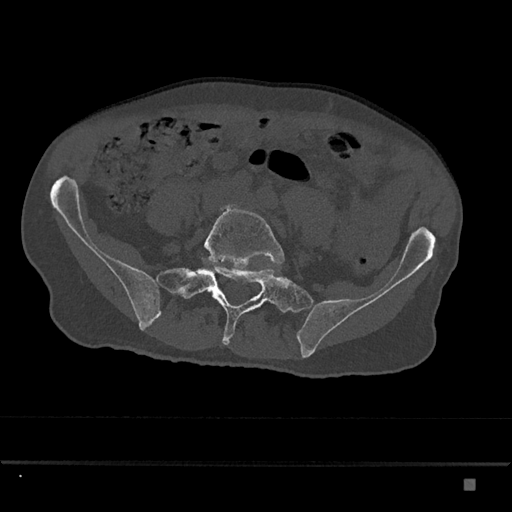
CT including the spine, one axial slice. Slice 249 of 797 in the series (ordered by position). Reconstruction kernel Br40s/3. Bone window (W 1800 / L 400 HU). 0.5 mm slice thickness. 512 × 512 image matrix, field of view 390 × 390 mm. Male patient, age 72 years. From the clinical record (not read from this slice): primary cancer: prostate.
Structures marked on this image (semi-automatically segmented with operator editing):
- L5 vertebra: bounding box <204,205,284,271> (left, top, right, bottom; pixels)